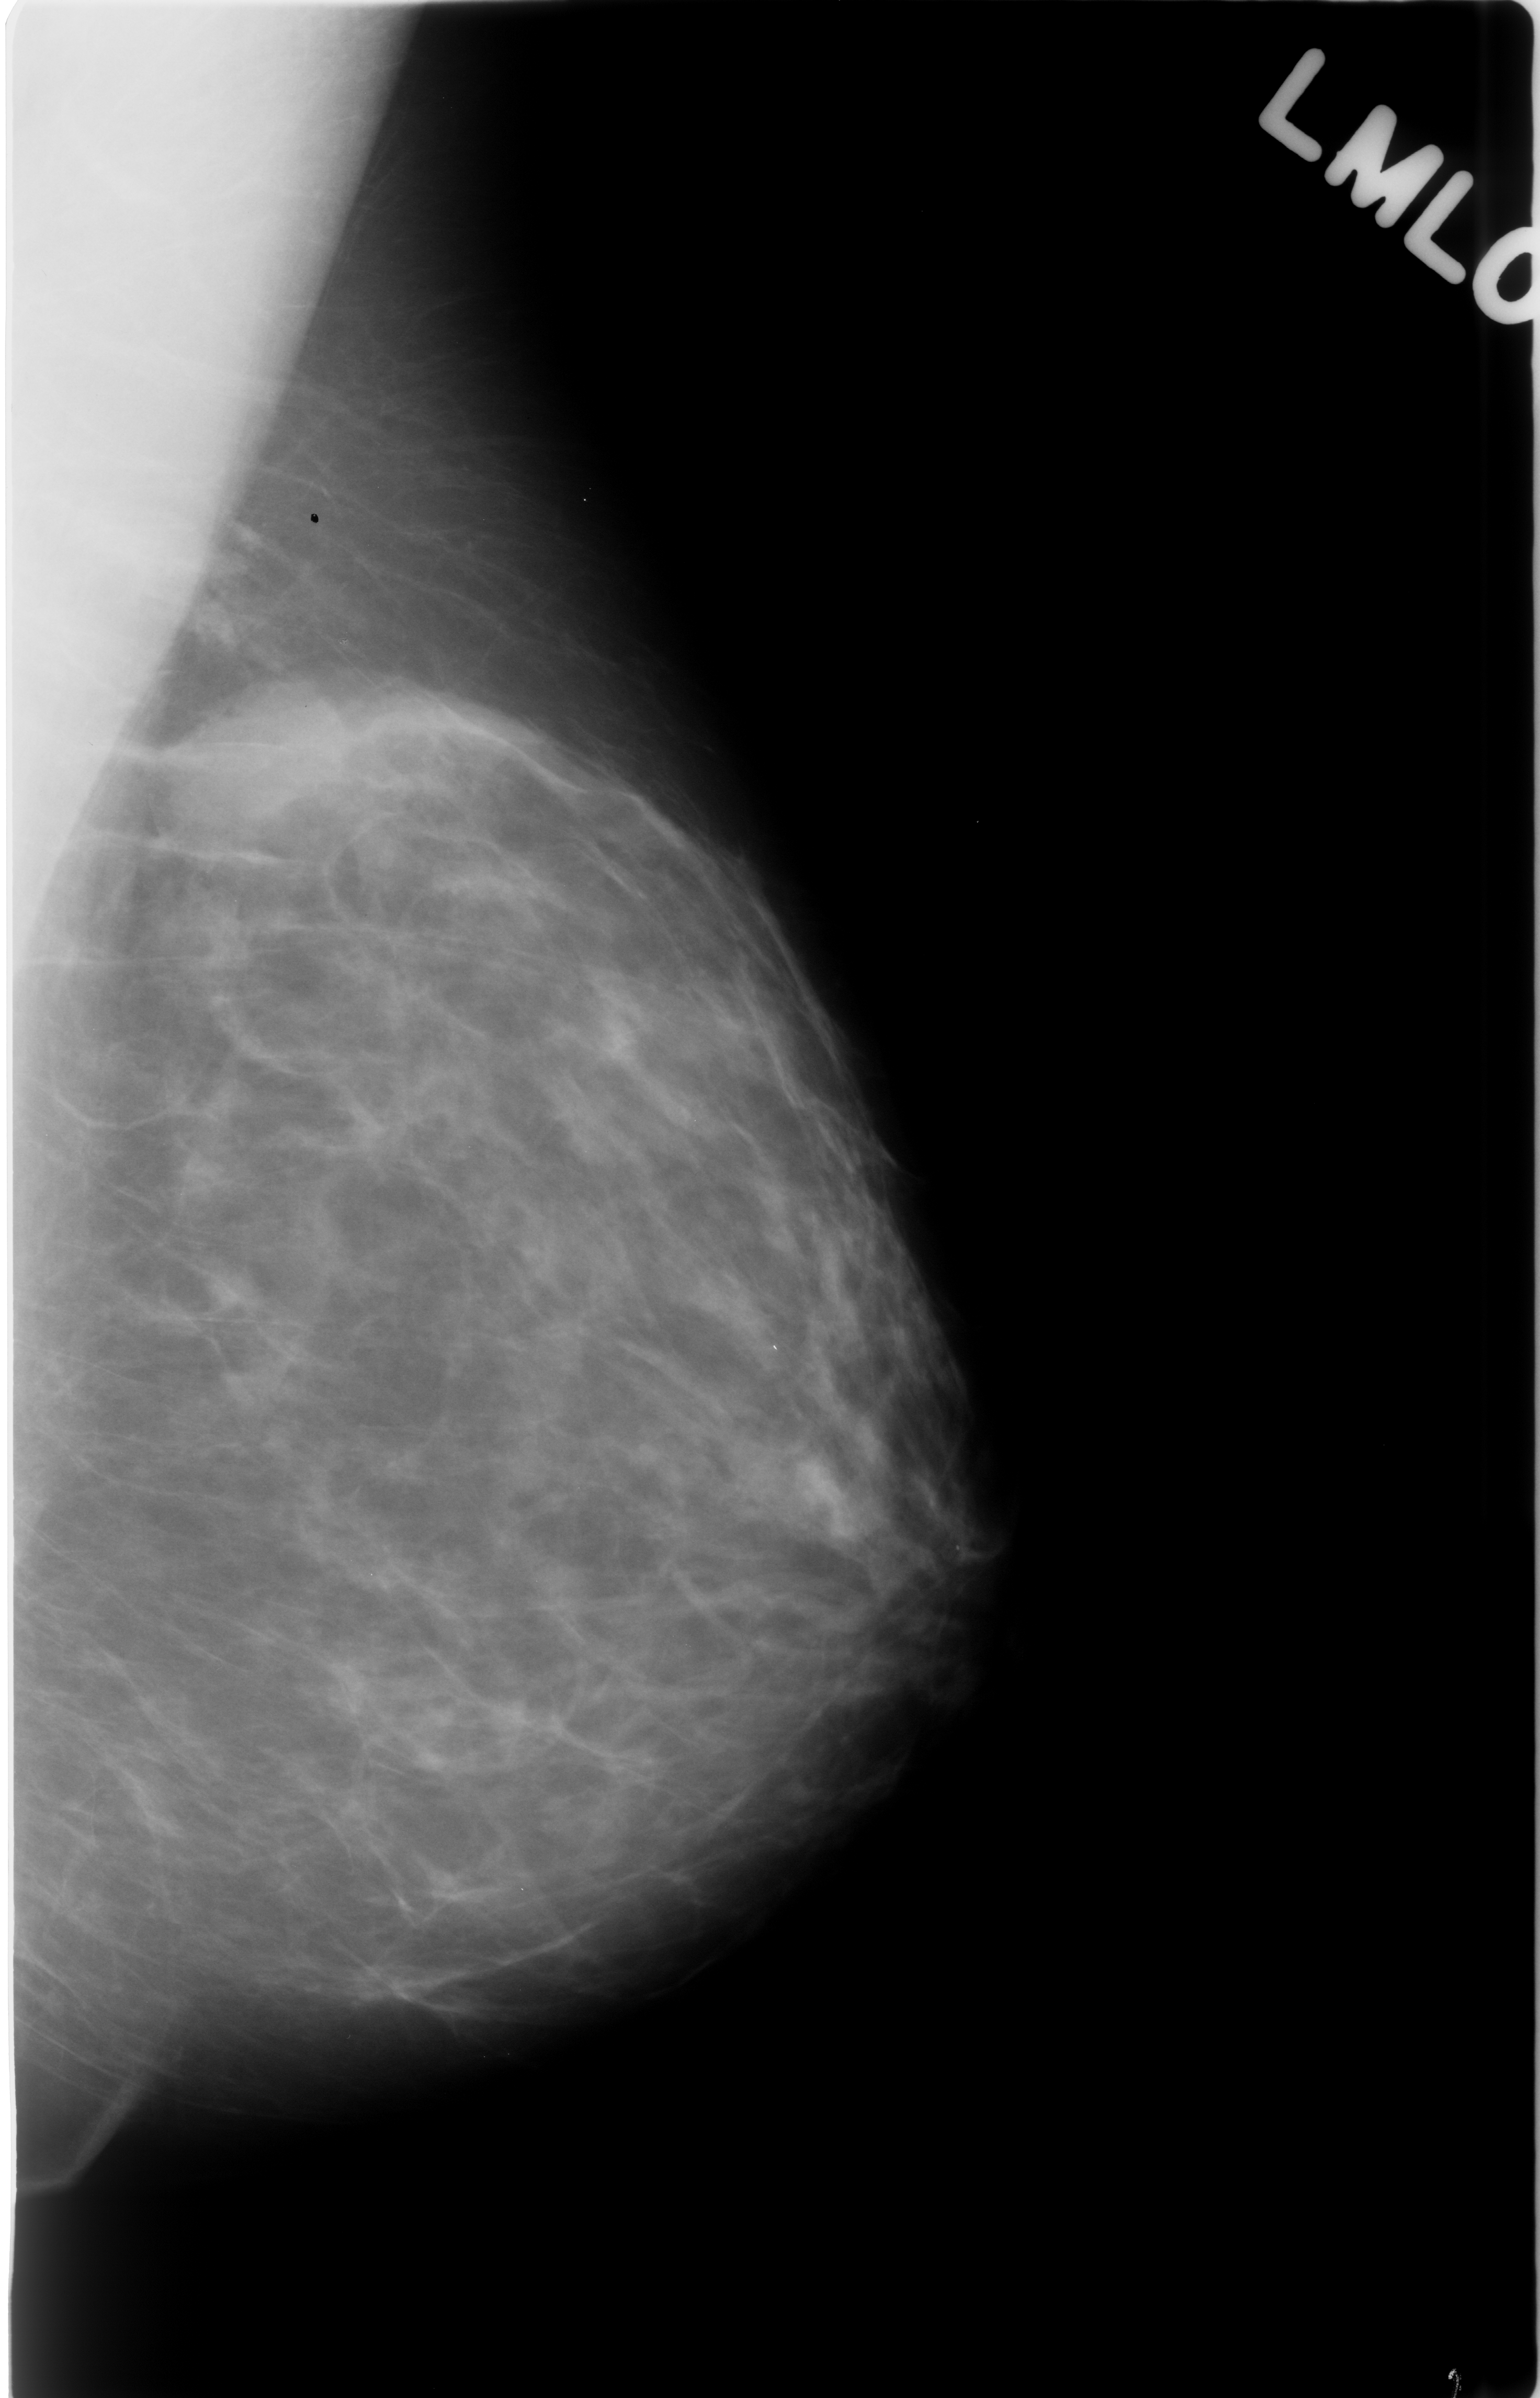
Mammogram (digitized film). Left breast. Mediolateral oblique (MLO) view. BI-RADS breast density category 1 (scale 1–4). 1540 × 2398 image matrix.
Marked abnormalities (boxes around the expert regions of interest):
- mass, shape oval, margins ill defined; BI-RADS assessment category 3; outcome (as recorded, no biopsy): benign without callback (not worked up further): bounding box (x1, y1, x2, y2) in pixels: (207, 663, 459, 891)